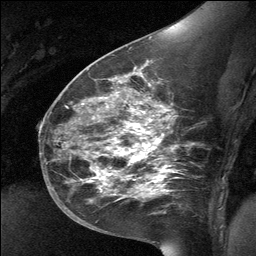
Breast MRI (dynamic contrast-enhanced), one sagittal slice. Slice 38 of 64 in the series (ordered by position). Dynamic contrast-enhanced study with each time point stored as its own series, time point 2 of 3 at this slice position (early post-contrast, ordered by acquisition time). 1.5 T. TE 4.8 ms, TR 27 ms. 2 mm slice thickness. 256 × 256 image matrix, field of view 200 × 200 mm. Patient: female, 39 years. From the clinical record (not read from this slice): setting: breast cancer imaged before/during neoadjuvant chemotherapy; receptor status: HER2-positive.
Outlined on this slice (semi-automatic segmentation, software-assisted and operator-edited):
- analysis volume of interest (the breast-tissue region the enhancement analysis was run in; not a lesion): box from (x=70, y=69) to (x=182, y=224) px
- tumour enhancement mask (voxels above the 90 % enhancement threshold inside the analysis volume of interest): (x=89, y=125)–(x=164, y=194)